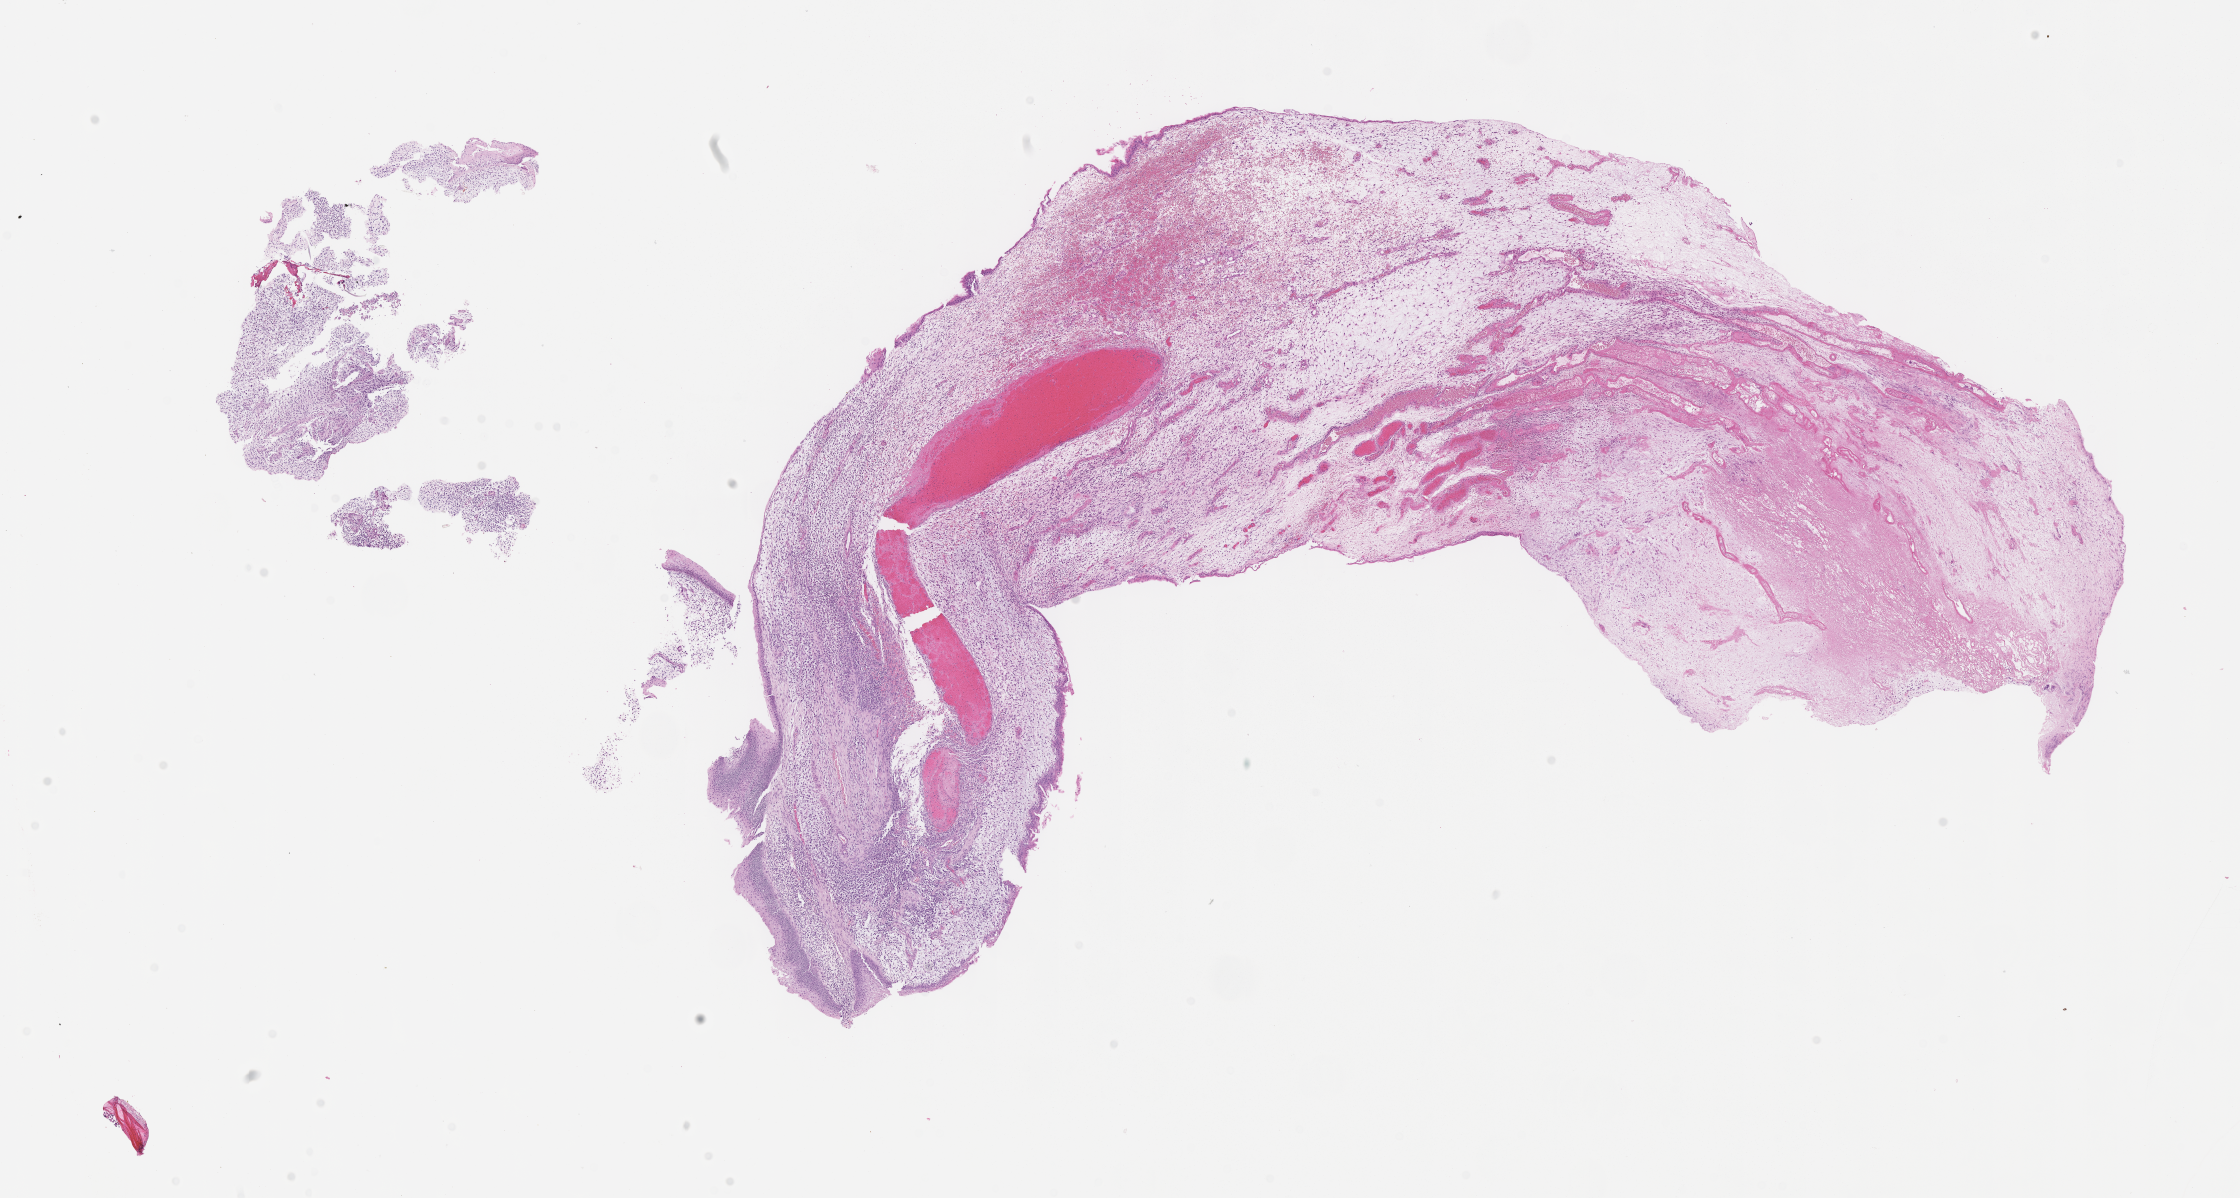
Haematoxylin and eosin whole-slide image of tumor tissue — shown as a low-resolution overview of the whole scanned area (about 18.1 x 9.7 mm); formalin-fixed paraffin-embedded section; site: vagina. Patient: female, age 1.8 years at diagnosis.
Diagnosis: rhabdomyosarcoma; histological classification: botryoid. Metastatic status at presentation (as recorded): non-metastatic. Stage (as recorded): 1.